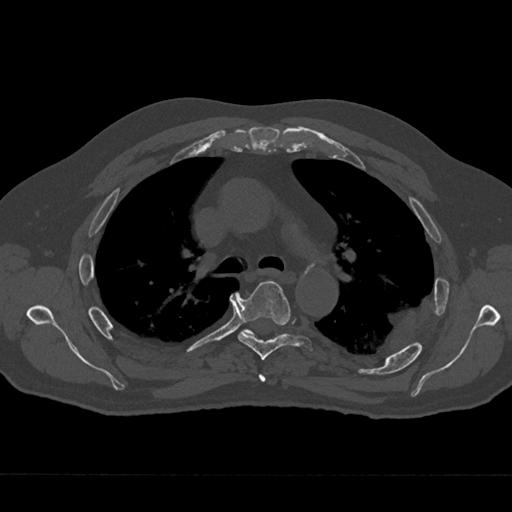
CT including the spine, one axial slice; slice 469 of 797 in the series (ordered by position); reconstruction kernel Br40s/3; 120 kVp; bone window (W 1800 / L 400 HU); 0.5 mm slice thickness; 512 × 512 image matrix, field of view 377 × 377 mm. Patient: male, 75 years. From the clinical record (not read from this slice): primary cancer: renal; vertebrae with lytic lesions (as recorded): T4.
Structures marked on this image (semi-automatically segmented with operator editing):
- T4 vertebra: bounding box <259,374,266,382> (left, top, right, bottom; pixels)
- T5 vertebra: <236,281,313,360>
- T6 vertebra: <243,329,254,335>